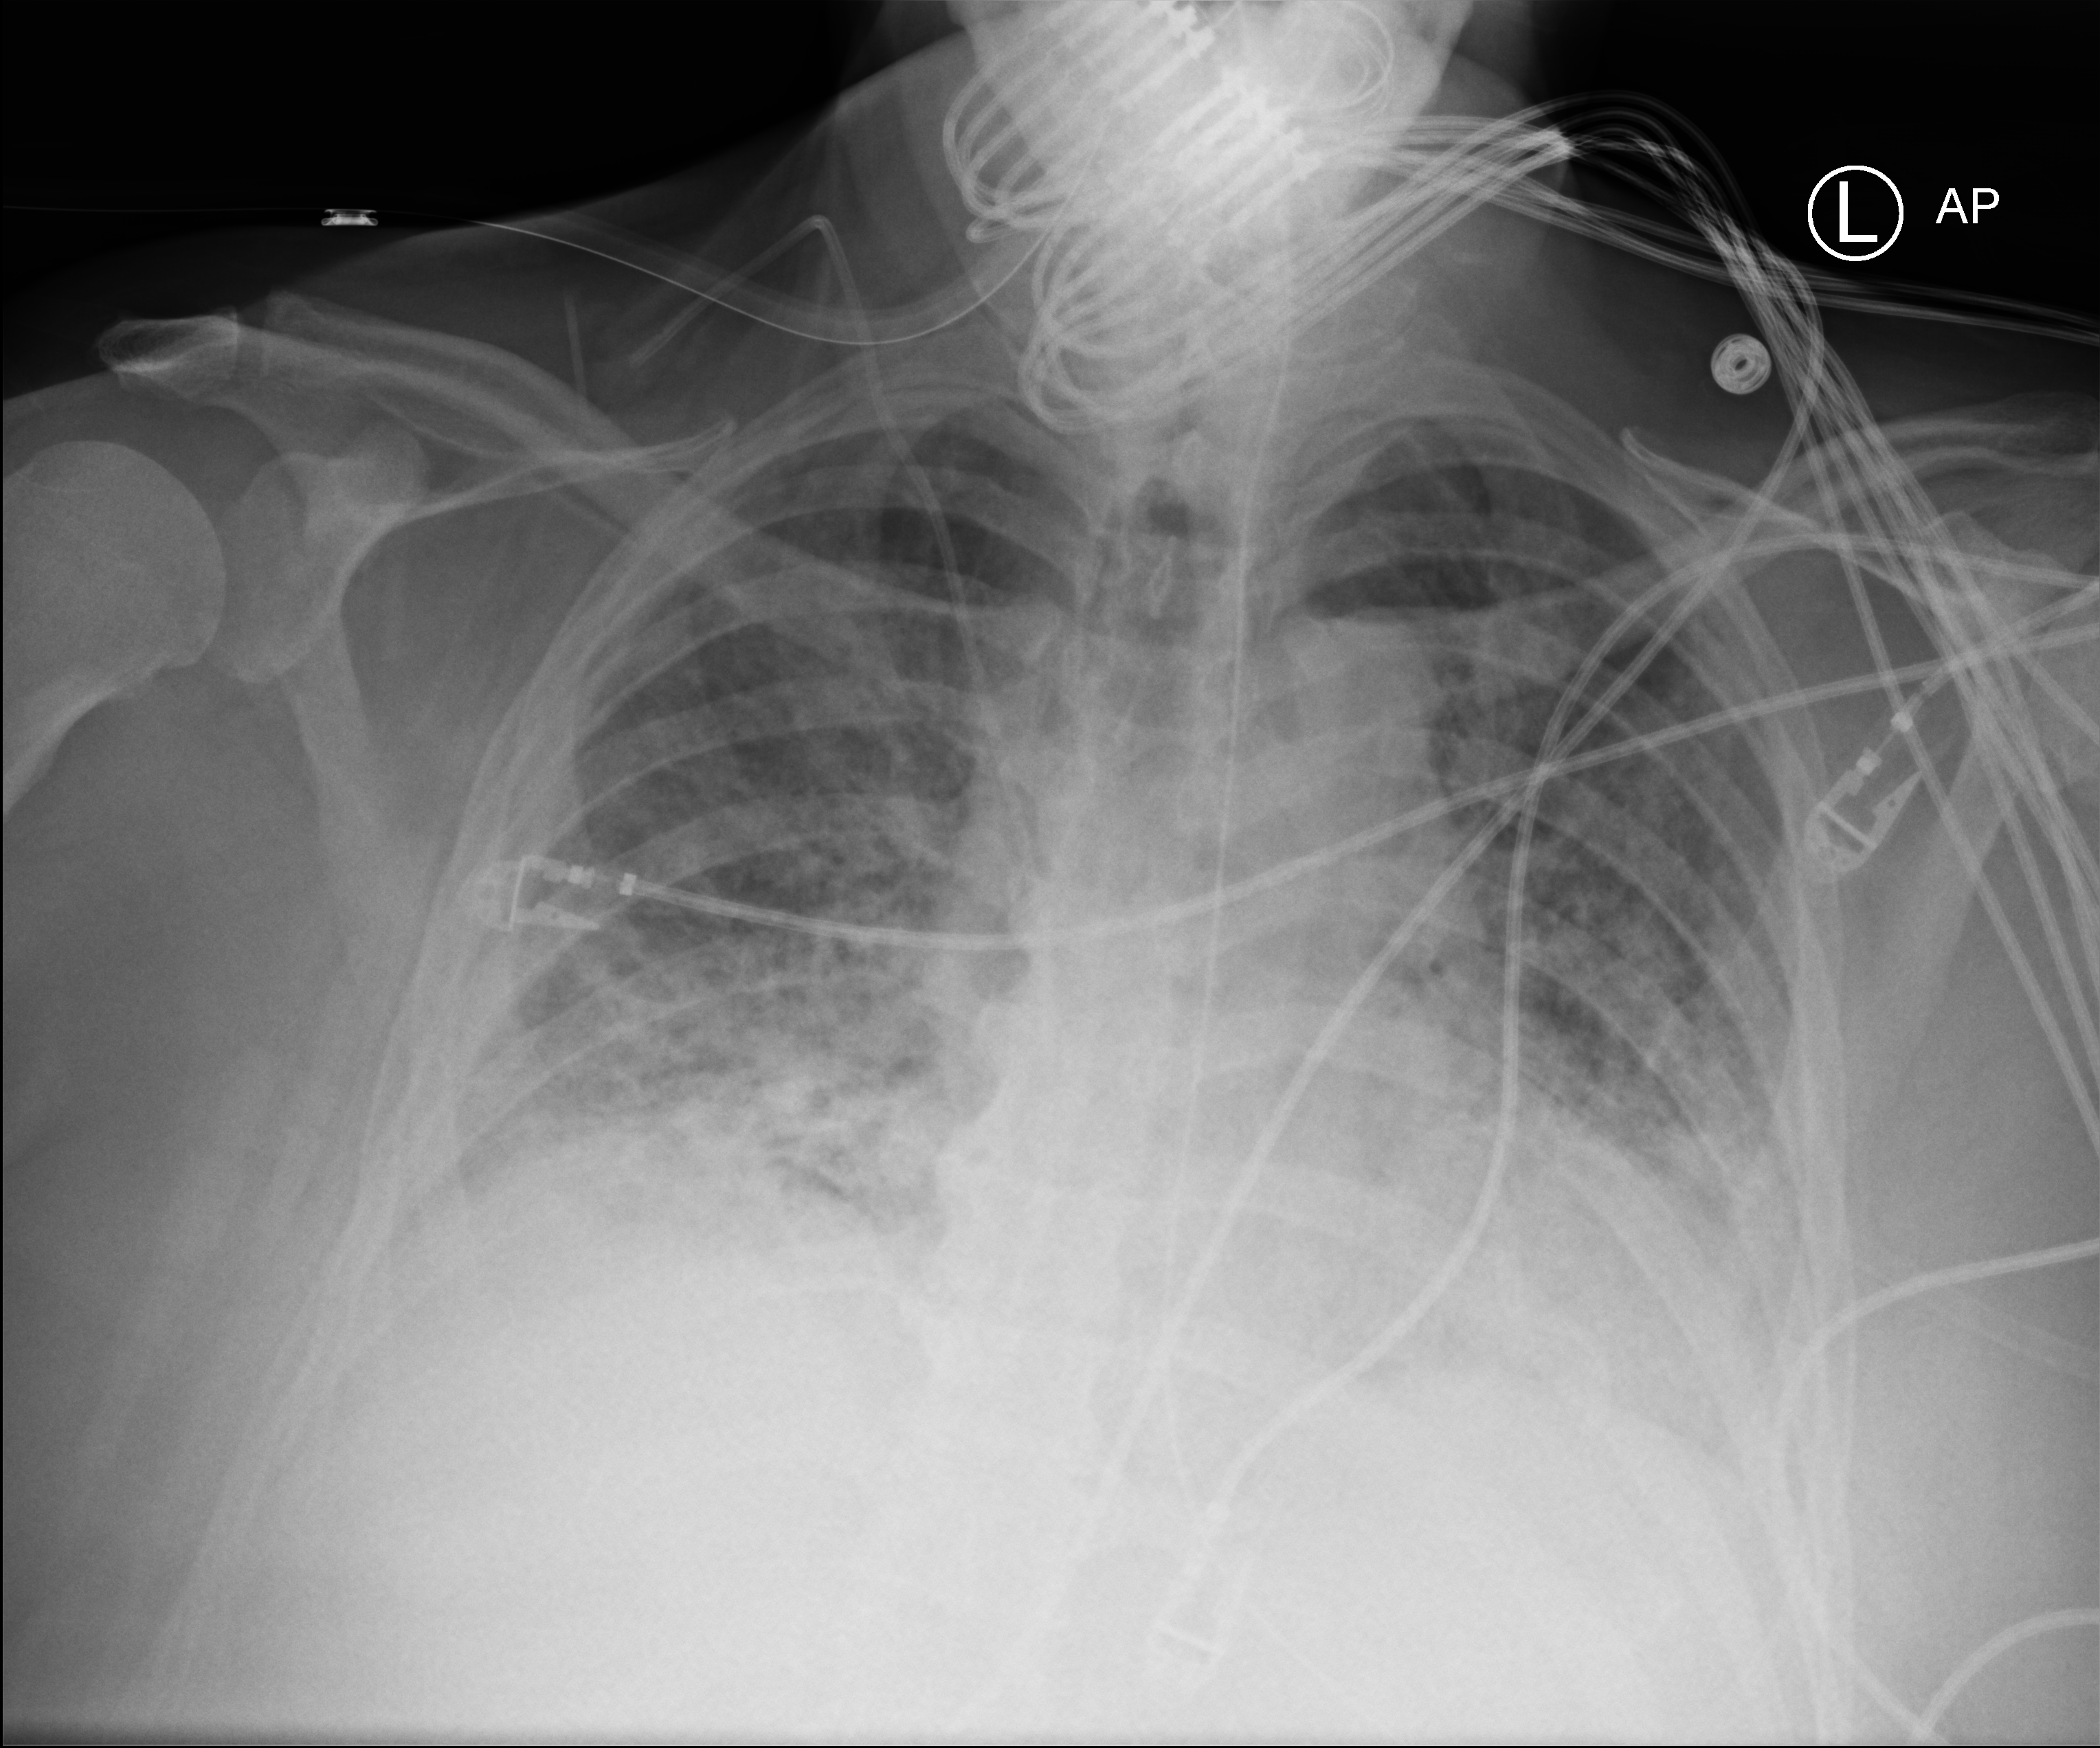
Bedside chest radiograph (computed radiography); anteroposterior (AP) projection. Patient hospitalised with COVID-19; male, aged 60–74 years.
Hospital-stay facts (about this admission, not read from this image; timing relative to this image not recorded): mechanically ventilated during this hospital stay: yes.